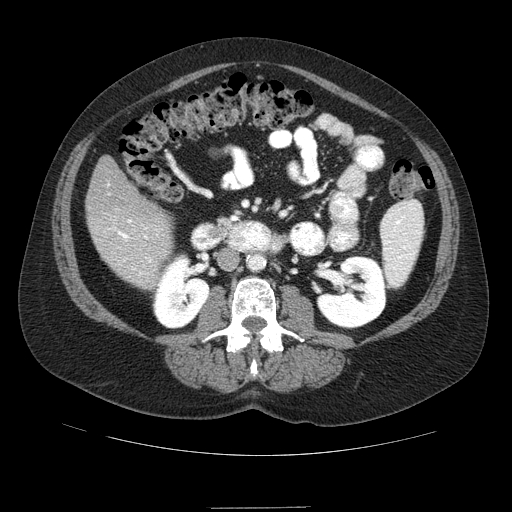
Contrast-enhanced abdominal CT (liver protocol), one axial slice; slice 24 of 89 in the series (ordered by position); reconstruction kernel STANDARD; soft-tissue window (W 400 / L 40 HU); 512 × 512 image matrix, field of view 400 × 400 mm. From the clinical record (not read from this slice): diagnosis: hepatocellular carcinoma (patient treated with transarterial chemoembolisation; whether this scan precedes or follows treatment is not stated here); TNM stage (as recorded): Stage-IIIB; Child-Pugh class: A; tumour nodularity: multinodular.
Outlined on this slice (semi-automatically segmented with operator editing):
- liver parenchyma outside the tumour (the mass and vessels are separate outlines, so this box may not span the whole liver): bounding box <86,156,172,288> (left, top, right, bottom; pixels)
- liver vessels: <118,219,151,275>